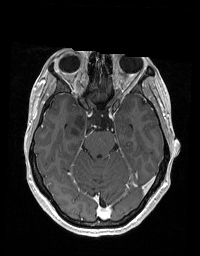
Brain MRI from a brain-tumour surgery series, one axial slice. Slice 121 of 192 in the series (ordered by position). T1-weighted post-contrast. 1 mm slice thickness. 200 × 256 image matrix, field of view 195 × 250 mm. From the clinical record (not read from this slice): histopathology: Glioblastoma; WHO grade: 2; IDH mutation: no; tumour location: Right Skull Base Temporal.
Structures marked on this image (expert manual segmentation):
- tumour: bounding box (x1, y1, x2, y2) in pixels: (72, 113, 102, 135)